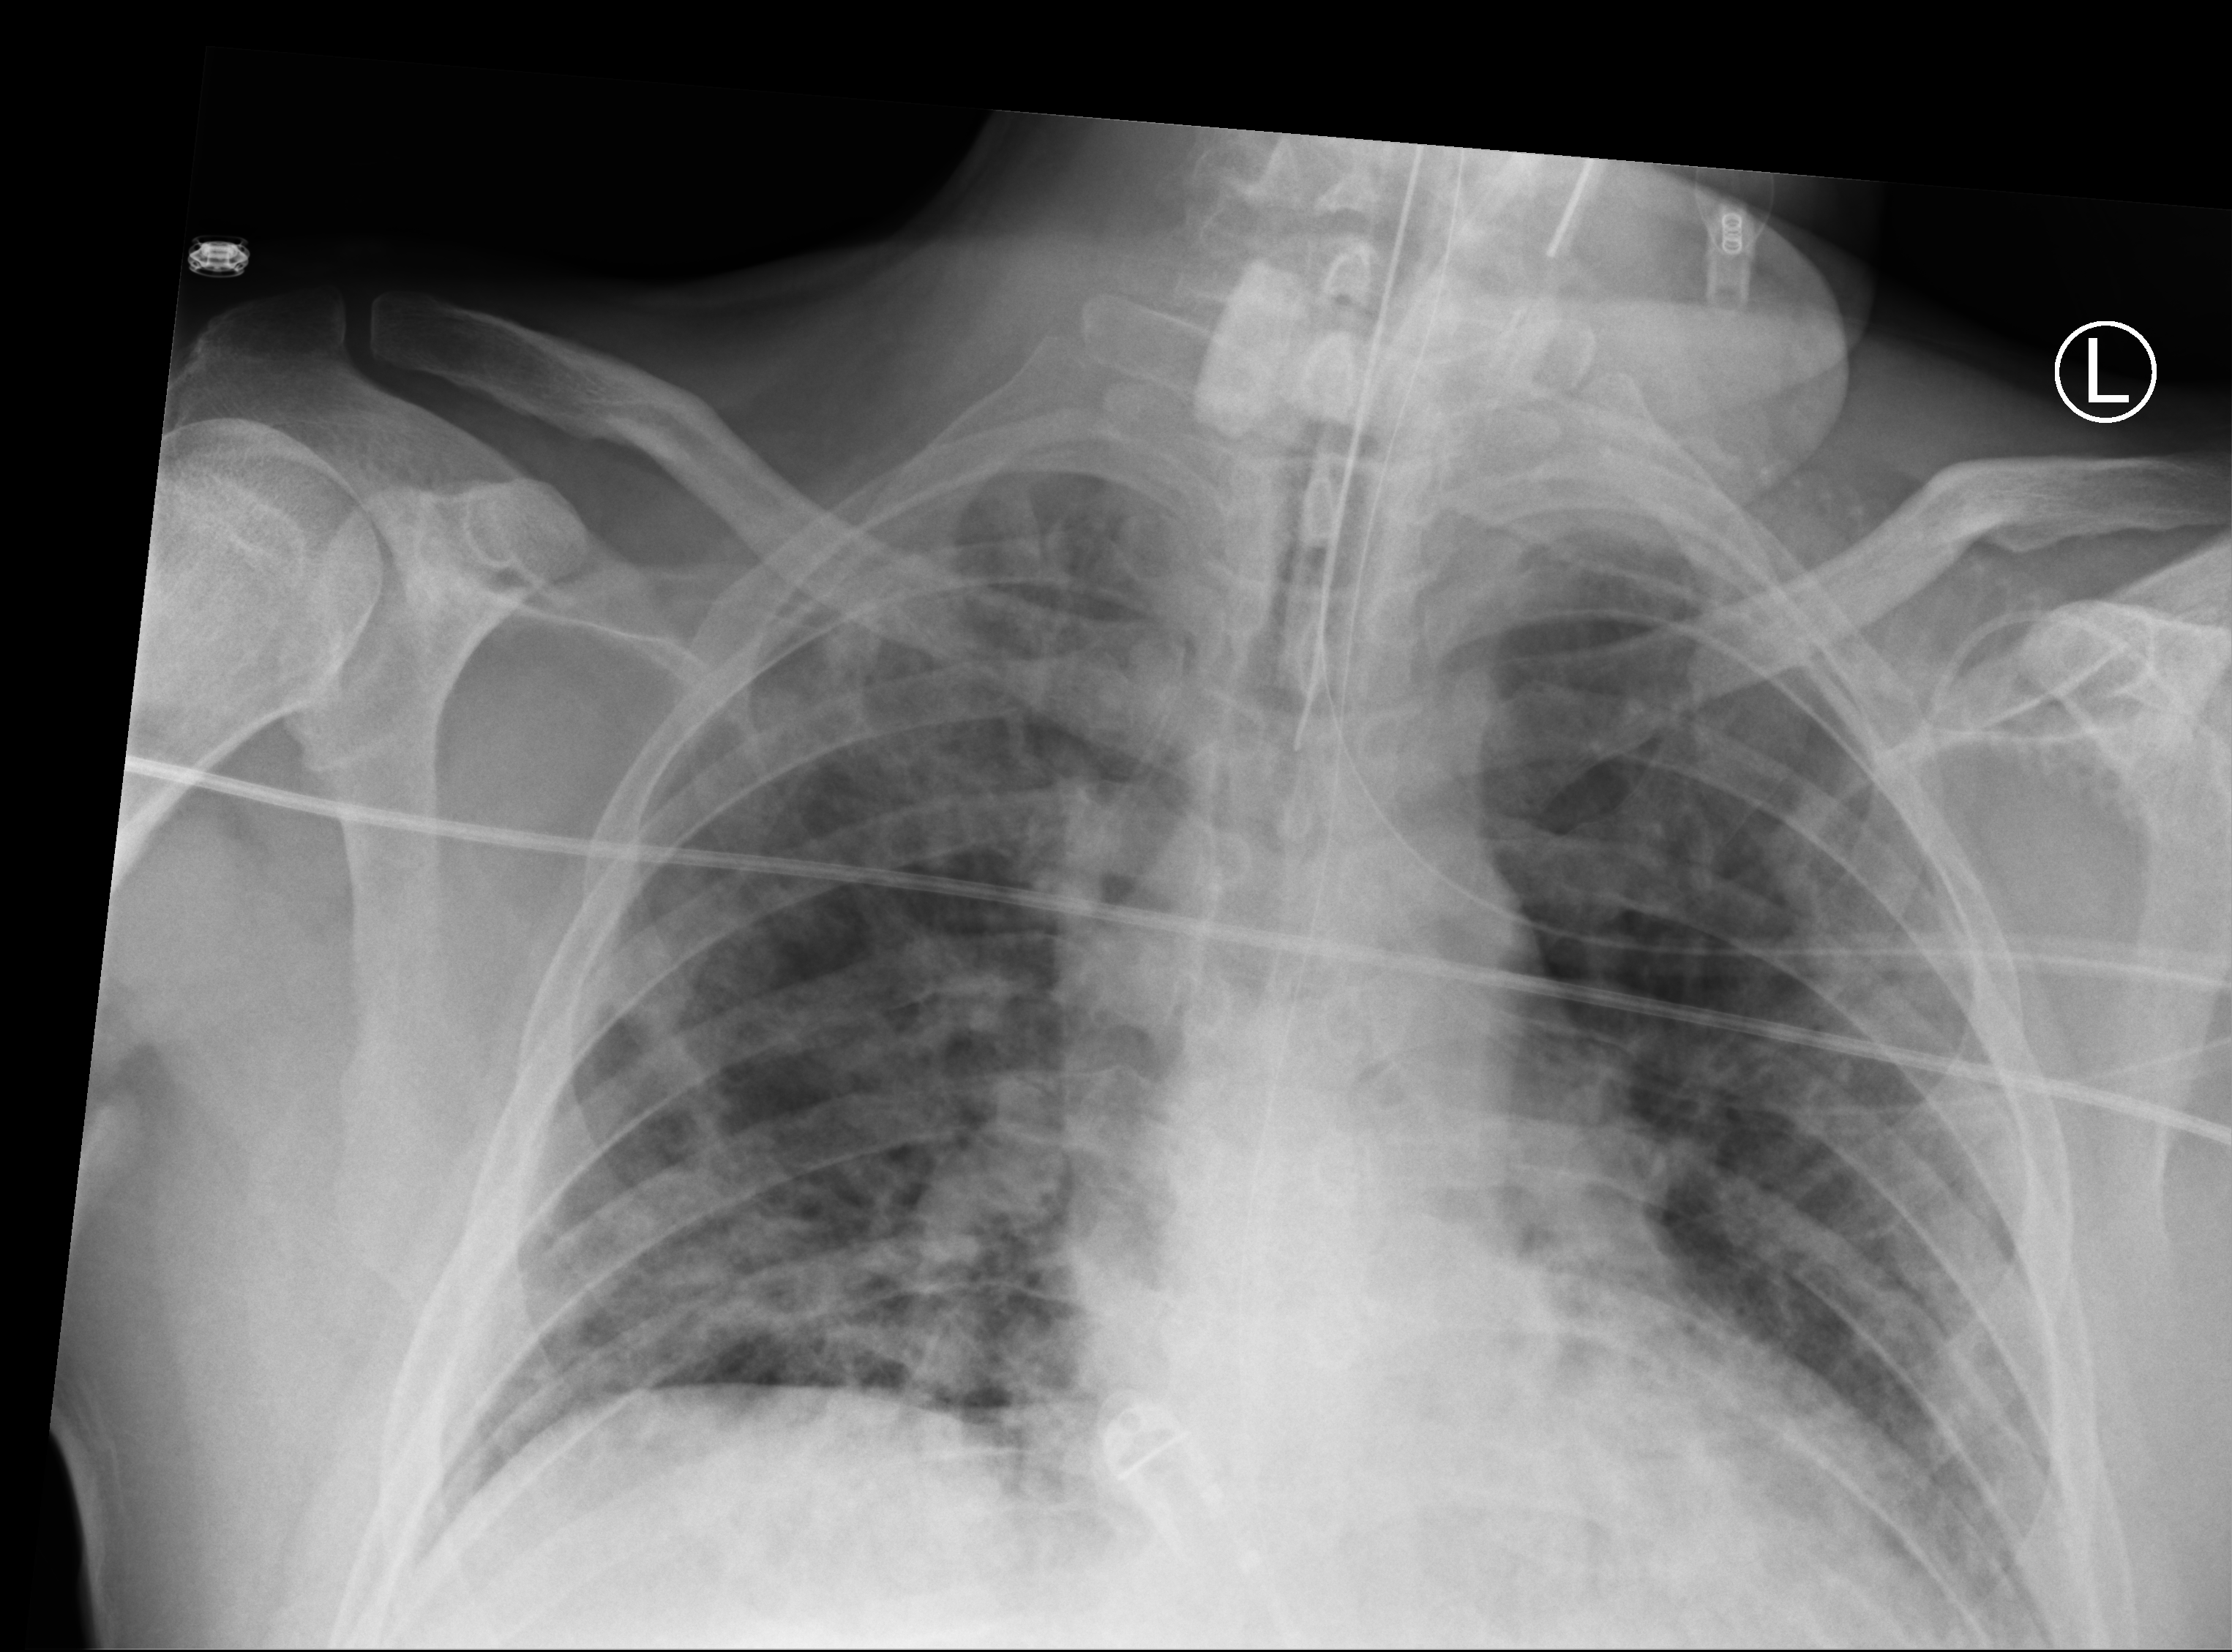
Chest X-ray (portable), anteroposterior (AP) projection. Patient hospitalised with COVID-19; male, aged 18–59 years.
From the hospital-stay record, not from the radiograph (when in the stay this image was taken is not recorded): mechanically ventilated during this hospital stay: yes; admitted to intensive care during this hospital stay: no.